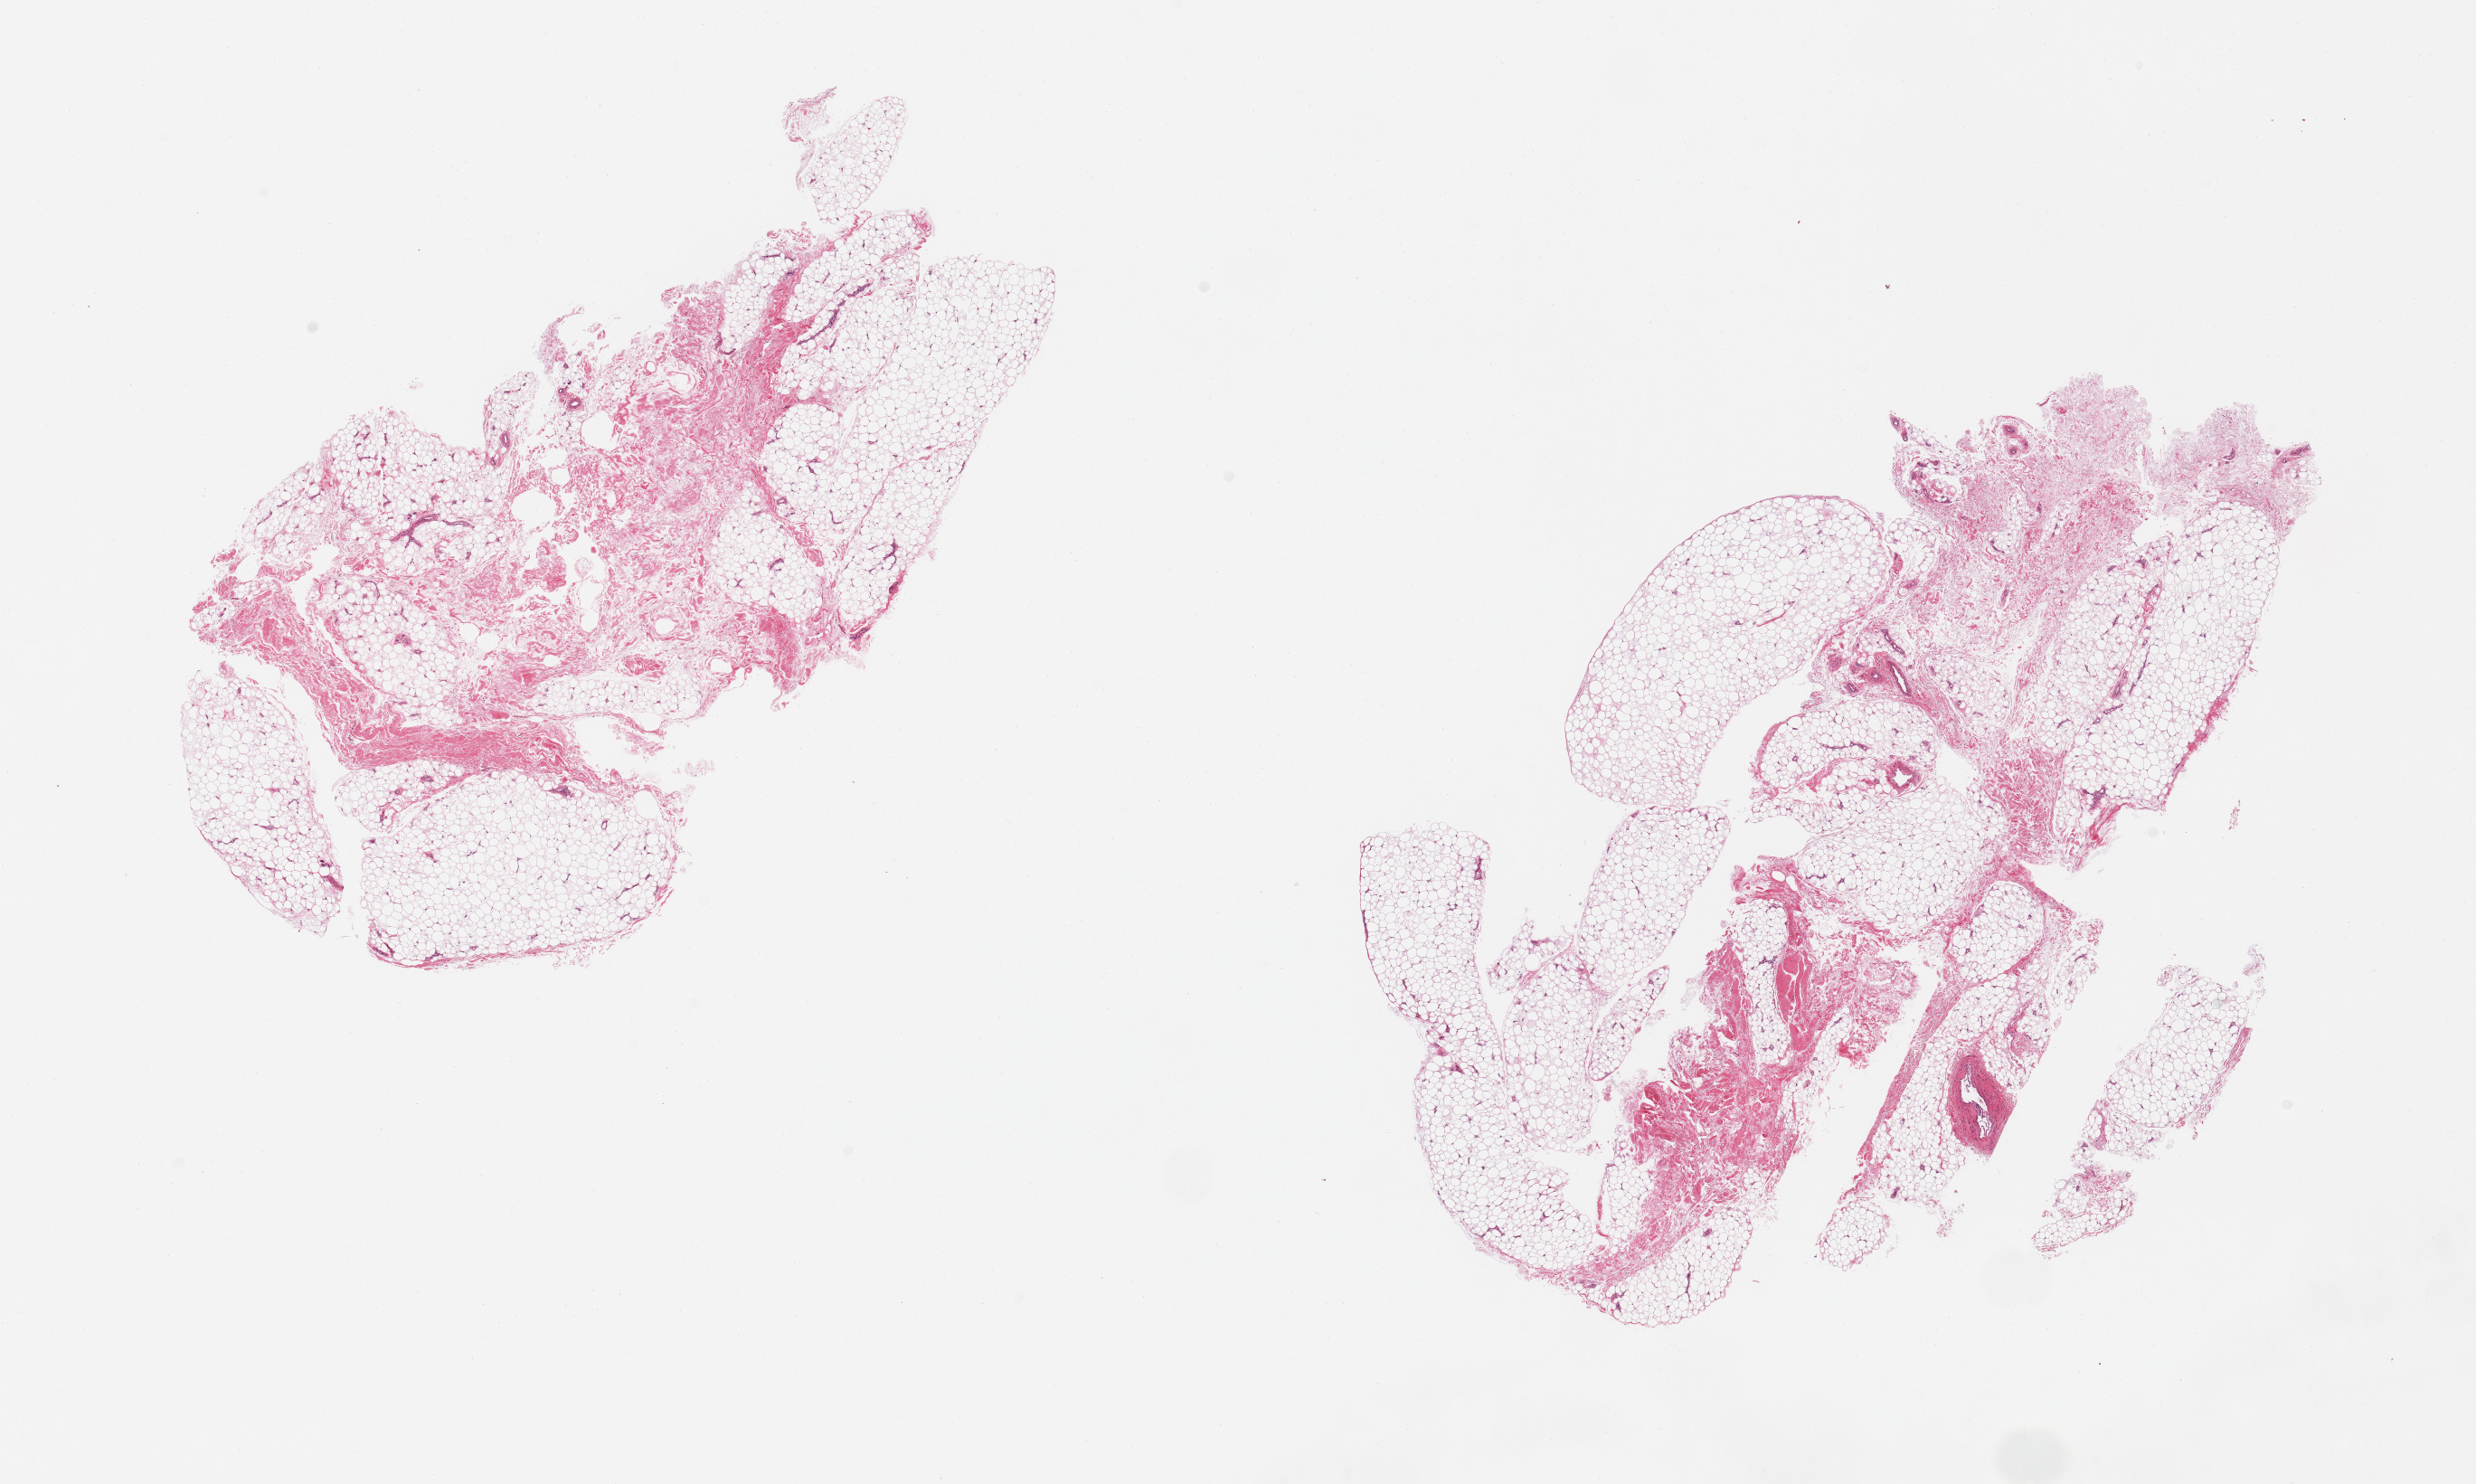
Haematoxylin and eosin whole-slide image — low-resolution overview of the scanned area, about 21.7 x 13.0 mm (from a 20x scan); PAXgene-fixed, paraffin-embedded tissue; target tissue: adipose tissue; donor tissue sample. Donor: male.
- reviewer comment on this tissue sample: 2 pieces, ~15-20% vascular/fascia elements